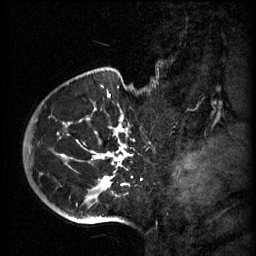
Breast MRI (dynamic contrast-enhanced), one sagittal slice. Position 48 of 60 along the scan axis. 3 images stored at this slice position (order not interpretable as contrast timing). 1.5 T. TE 4.2 ms, TR 11 ms. 2 mm slice thickness. 256 × 256 image matrix, field of view 200 × 200 mm. Patient: female, 51 years.
Annotated regions visible in this slice (semi-automatically segmented with operator editing):
- analysis volume of interest (the breast-tissue region the enhancement analysis was run in; not a lesion): bounding box [x1, y1, x2, y2] px = [48, 82, 154, 197]
- tumour enhancement mask (voxels above the 70 % enhancement threshold inside the analysis volume of interest): [61, 94, 132, 189]